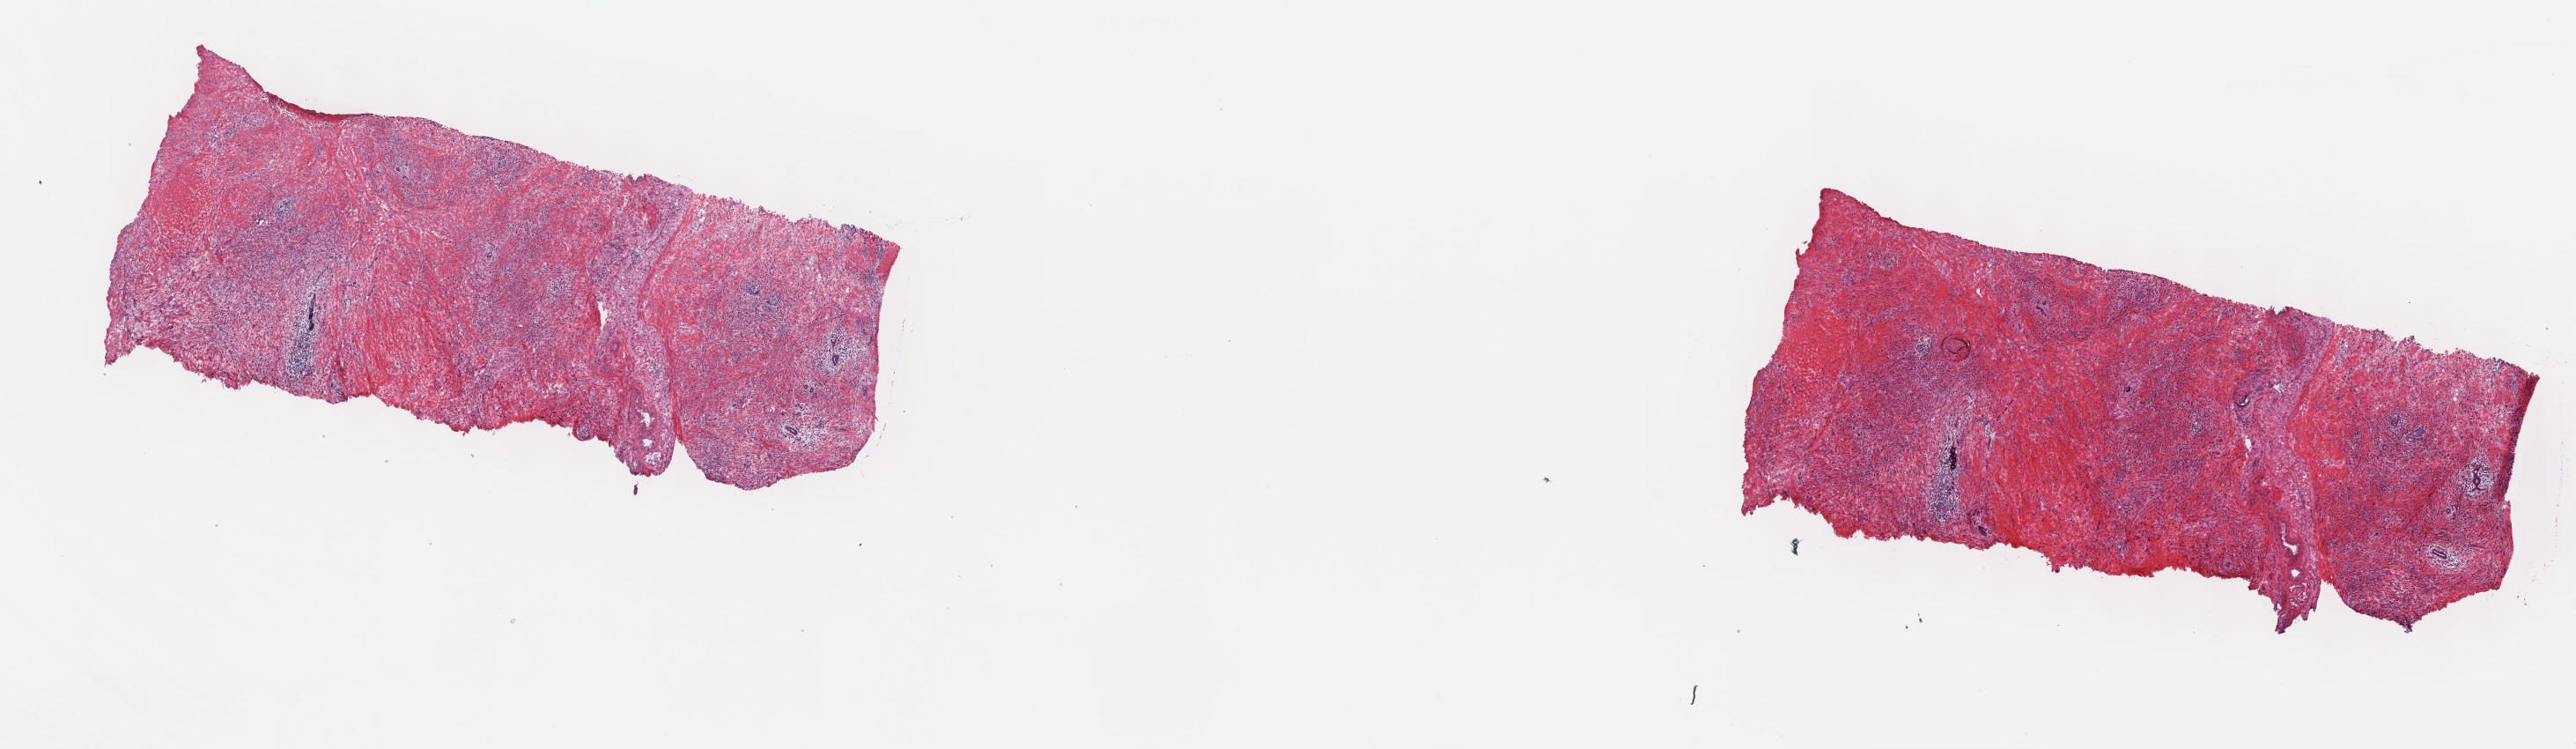
Whole-slide histology image, H&E — shown as a low-resolution overview of the whole scanned area (about 23.7 x 6.9 mm); frozen section; sample: primary tumour, breast. Patient: female, age at initial diagnosis 55 years. Slide review estimates, as recorded: tumour cells 60%, tumour nuclei 60%, normal cells 0%, stromal cells 40%, necrosis 0%. Inflammatory infiltration, as recorded: lymphocyte infiltration 40%, monocyte infiltration 20%, neutrophil infiltration 20%.
- AJCC pathologic stage: IIIA (7th edition)
- laterality: left
- lymph nodes positive (case pathology): 4 of 14 examined
- pathologic diagnosis: Lobular carcinoma, NOS